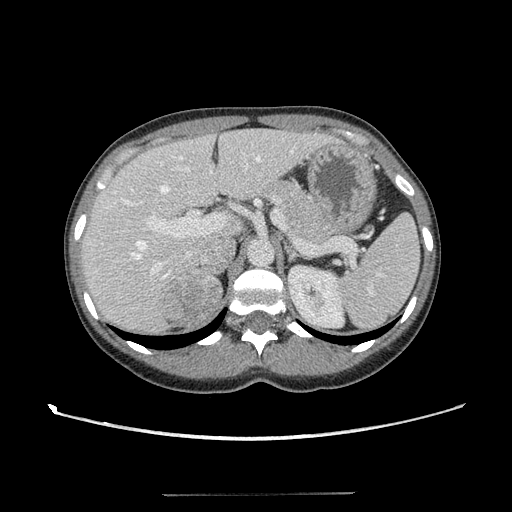
Contrast-enhanced abdominal CT, one axial slice; position 77 of 117 along the scan axis; reconstruction kernel STANDARD; 120 kVp; soft-tissue window (W 400 / L 40 HU); 2.5 mm slice thickness; 512 × 512 image matrix, field of view 365 × 365 mm. Female patient, age 35 years. Case-level facts recorded for this patient, not image findings: diagnosis: adrenocortical carcinoma; tumour side: right adrenal; tumour size at pathology: 3 cm; Ki-67 index: 21 %; stage (as recorded): 3.
Outlined on this slice (semi-automatically segmented with operator editing):
- mass: box from (x=161, y=276) to (x=221, y=325) px